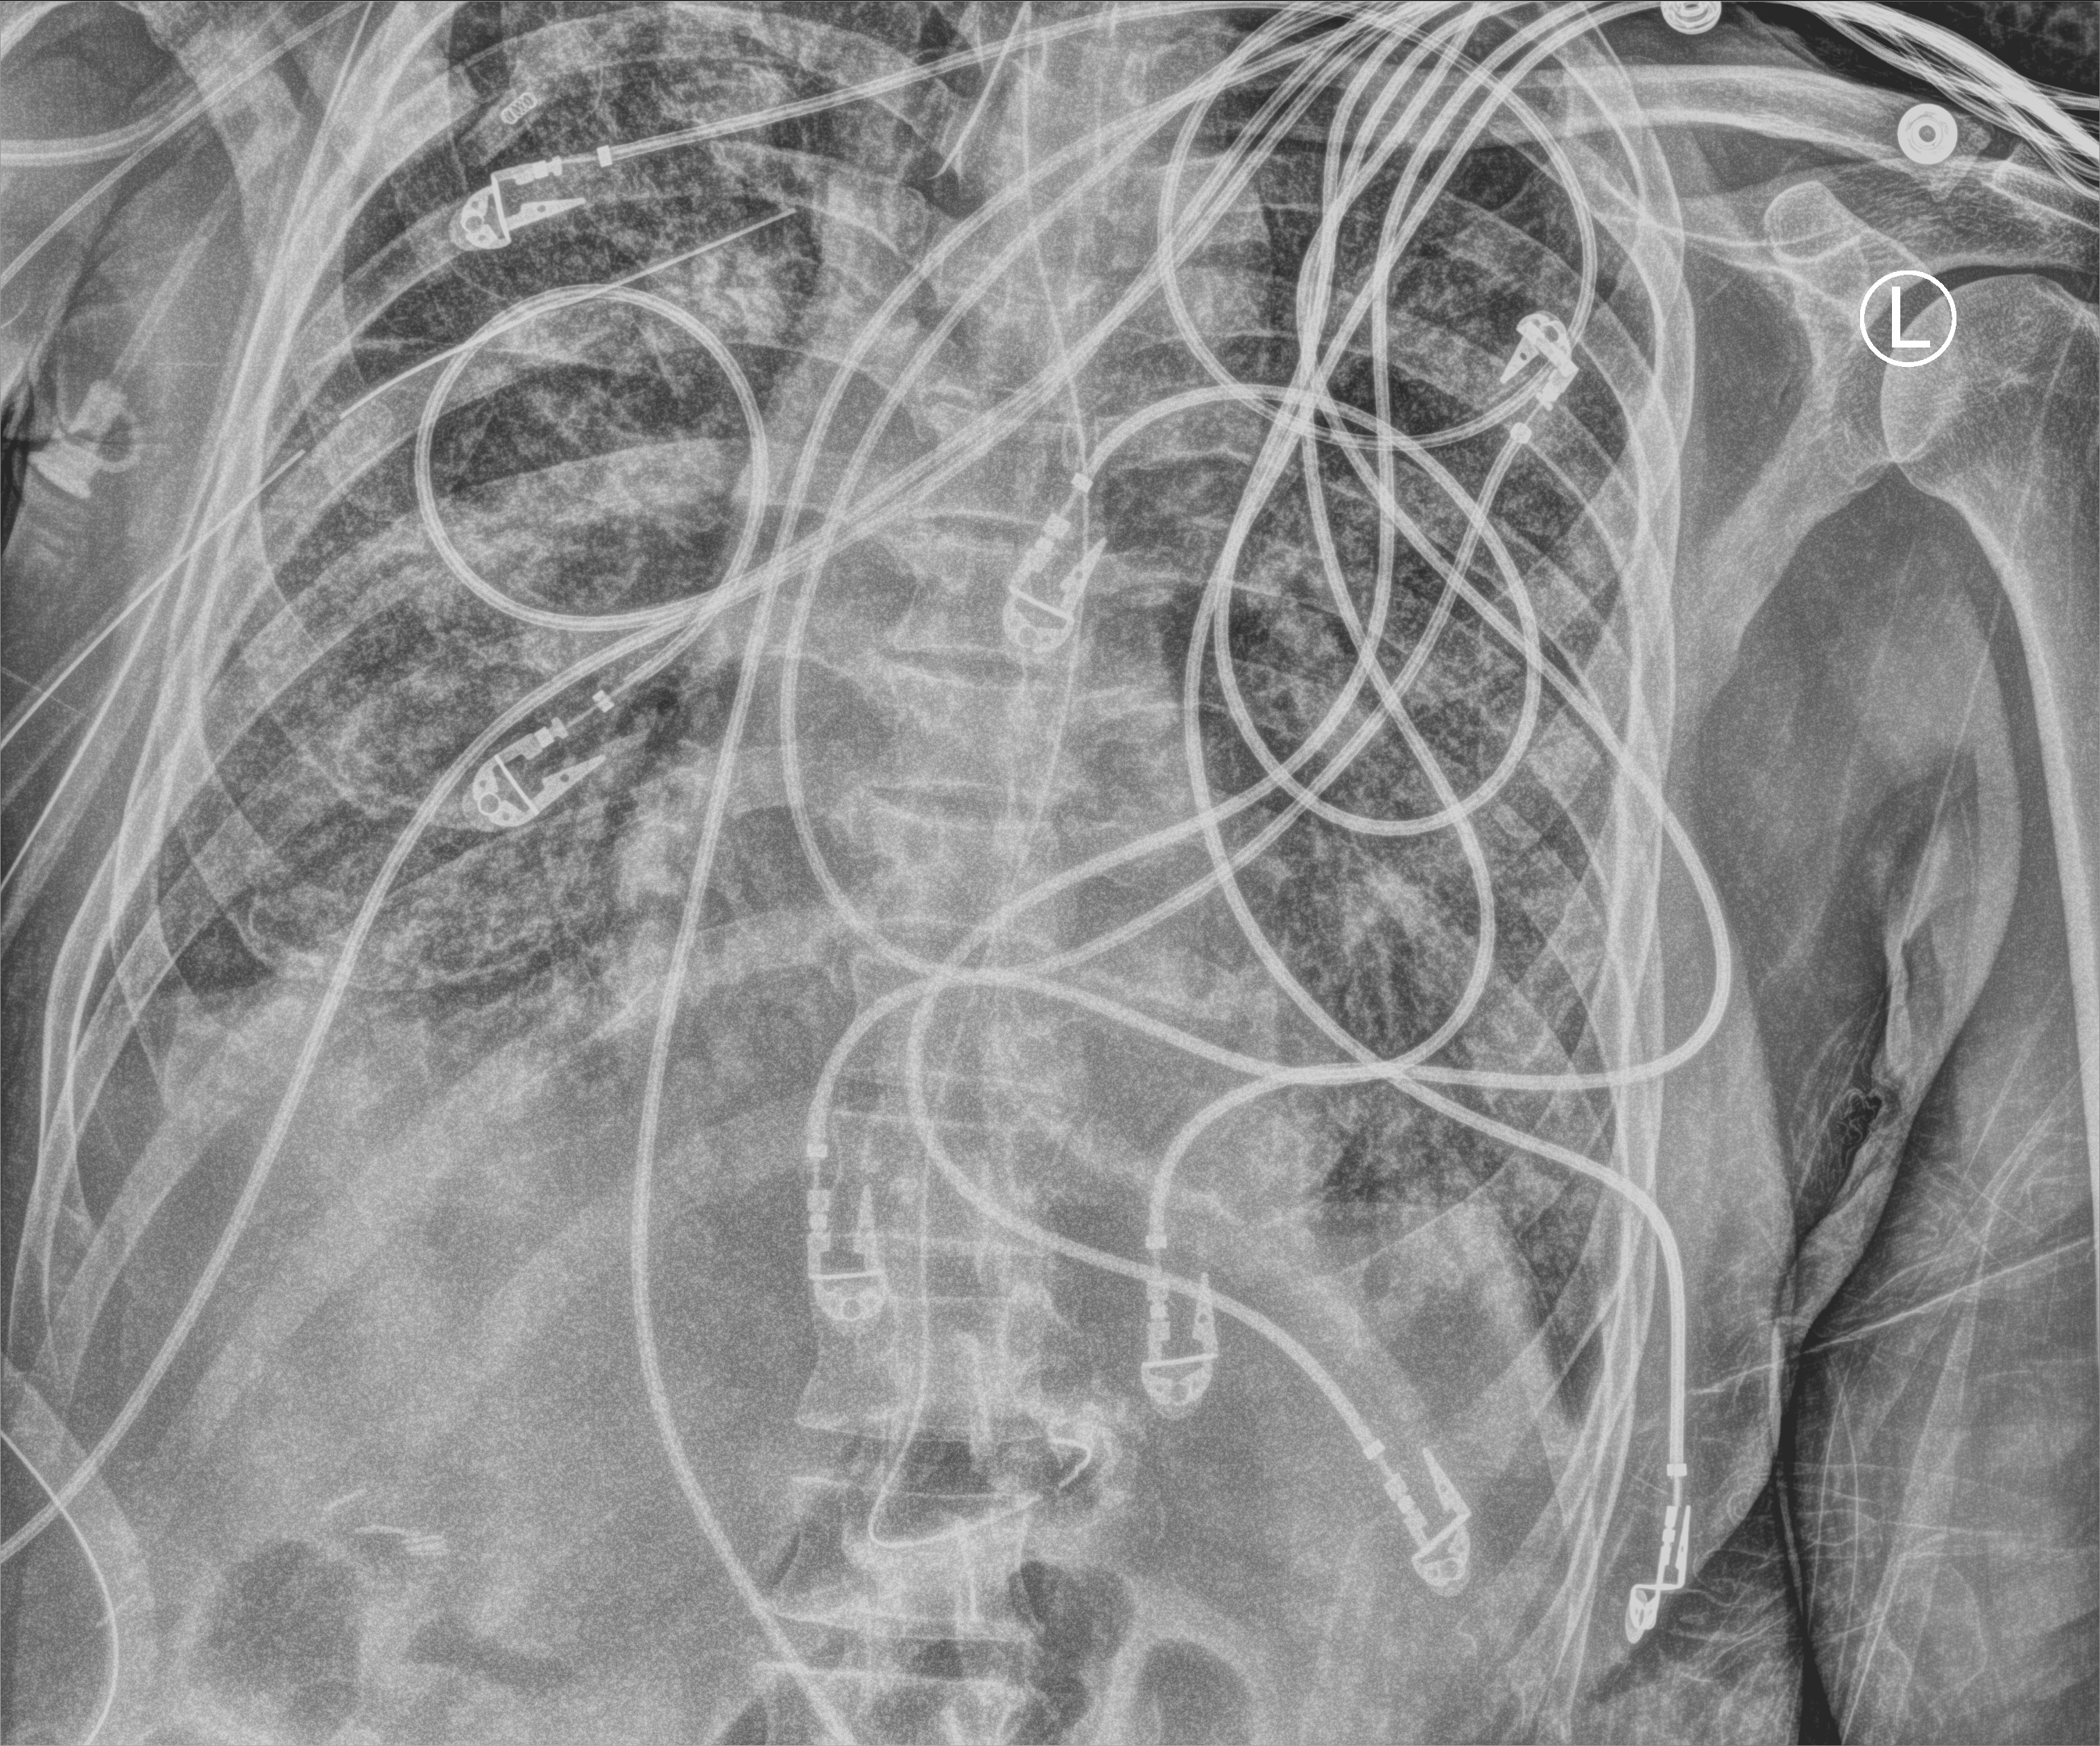
Portable chest radiograph; anteroposterior (AP) projection. Patient hospitalised with COVID-19; male, aged 60–74 years.
Hospital-stay facts (about this admission, not read from this image; timing relative to this image not recorded):
- mechanically ventilated during this hospital stay: yes
- admitted to intensive care during this hospital stay: yes